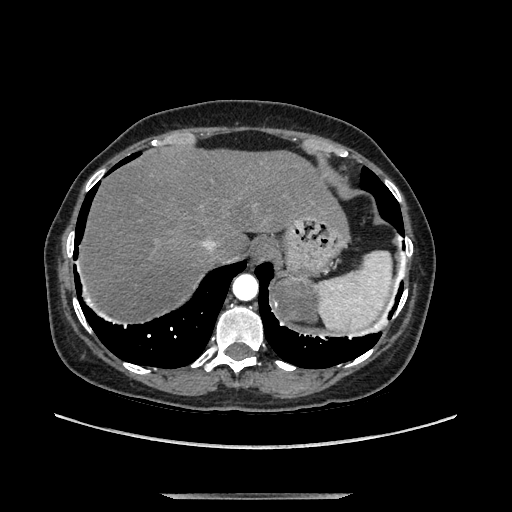
Contrast-enhanced abdominal CT, one axial slice; position 116 of 169 along the scan axis; soft-tissue window (W 400 / L 40 HU); 1.25 mm slice thickness; 512 × 512 image matrix. Female patient. From the clinical record (not read from this slice): diagnosis: adrenocortical carcinoma; tumour side: left adrenal; tumour size at pathology: 9 cm; Ki-67 index: 2 %; stage (as recorded): 3.
Annotated regions visible in this slice (semi-automatically segmented with operator editing):
- mass: bounding box [x1, y1, x2, y2] px = [277, 279, 315, 318]